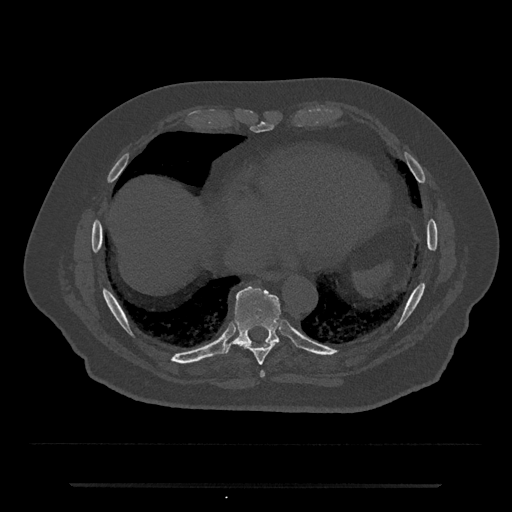
CT including the spine, one axial slice. Position 780 of 797 along the scan axis. Reconstruction kernel Br40s/3. 120 kVp. Bone window (W 1800 / L 400 HU). 512 × 512 image matrix, field of view 434 × 434 mm. Male patient, age 80 years. From the clinical record (not read from this slice): primary cancer: prostate; vertebrae with lytic lesions (as recorded): L1, T11.
Annotated regions visible in this slice (semi-automatic segmentation, software-assisted and operator-edited):
- T8 vertebra: bounding box (x1, y1, x2, y2) in pixels: (244, 342, 278, 365)
- T9 vertebra: (218, 287, 281, 357)